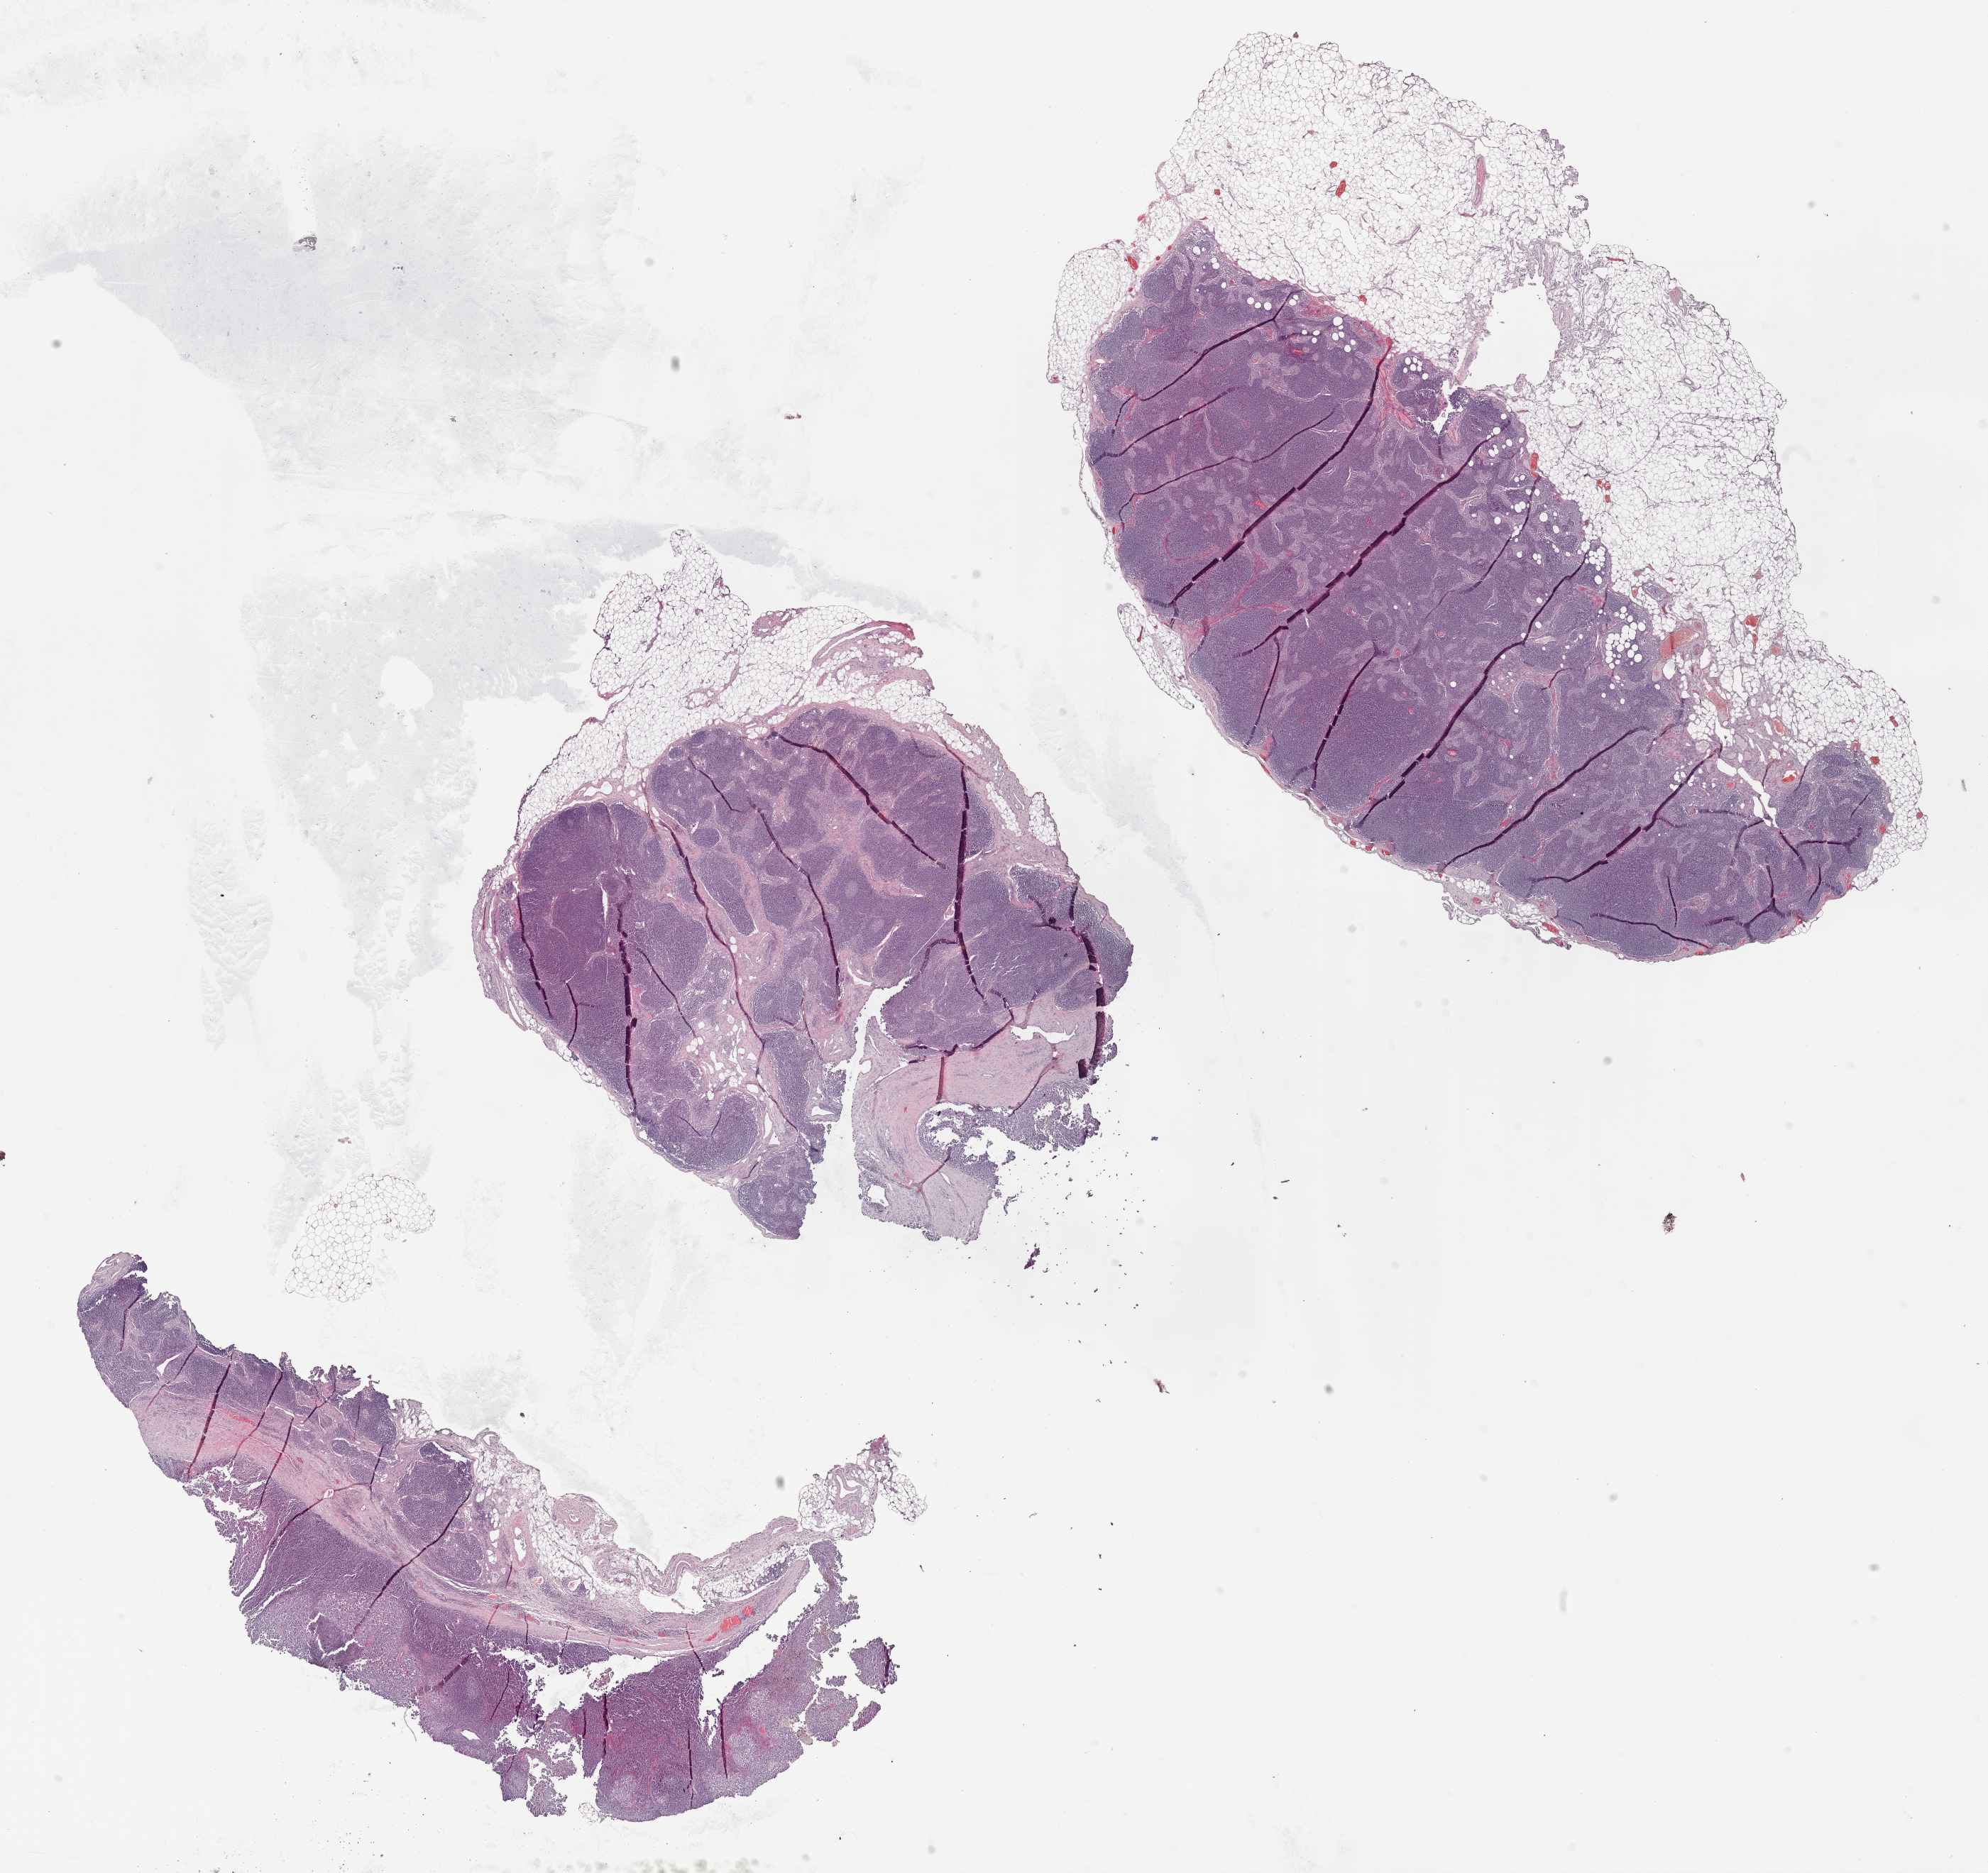
Whole-slide histology image, Hematoxylin and eosin (H&E) stained — shown as a low-resolution overview of the whole scanned area (about 22.7 x 21.3 mm, slide scanned at 40x); FFPE section; primary tumour sample from the skin. Patient: male, age at initial diagnosis 26 years.
Diagnosis: Malignant melanoma, NOS.